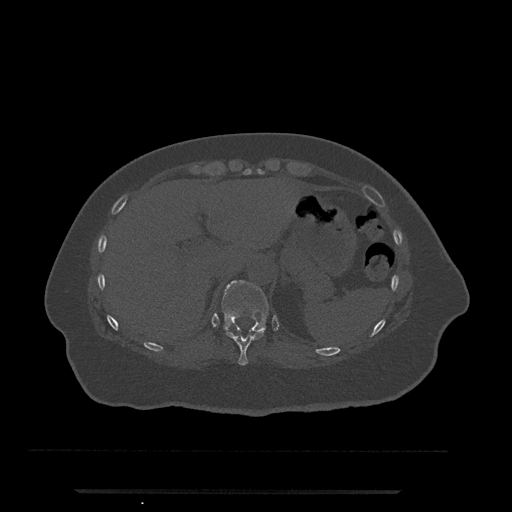
CT including the spine, one axial slice. Slice 255 of 797 in the series (ordered by position). 120 kVp. Bone window (W 1800 / L 400 HU). 0.5 mm slice thickness. 512 × 512 image matrix, field of view 440 × 440 mm. Patient: female, 51 years. From the clinical record (not read from this slice): primary cancer: neuro; vertebrae with lytic lesions (as recorded): T8.
Outlined on this slice (semi-automatically segmented with operator editing):
- T10 vertebra: bounding box <225,328,266,366> (left, top, right, bottom; pixels)
- T11 vertebra: <222,280,269,334>